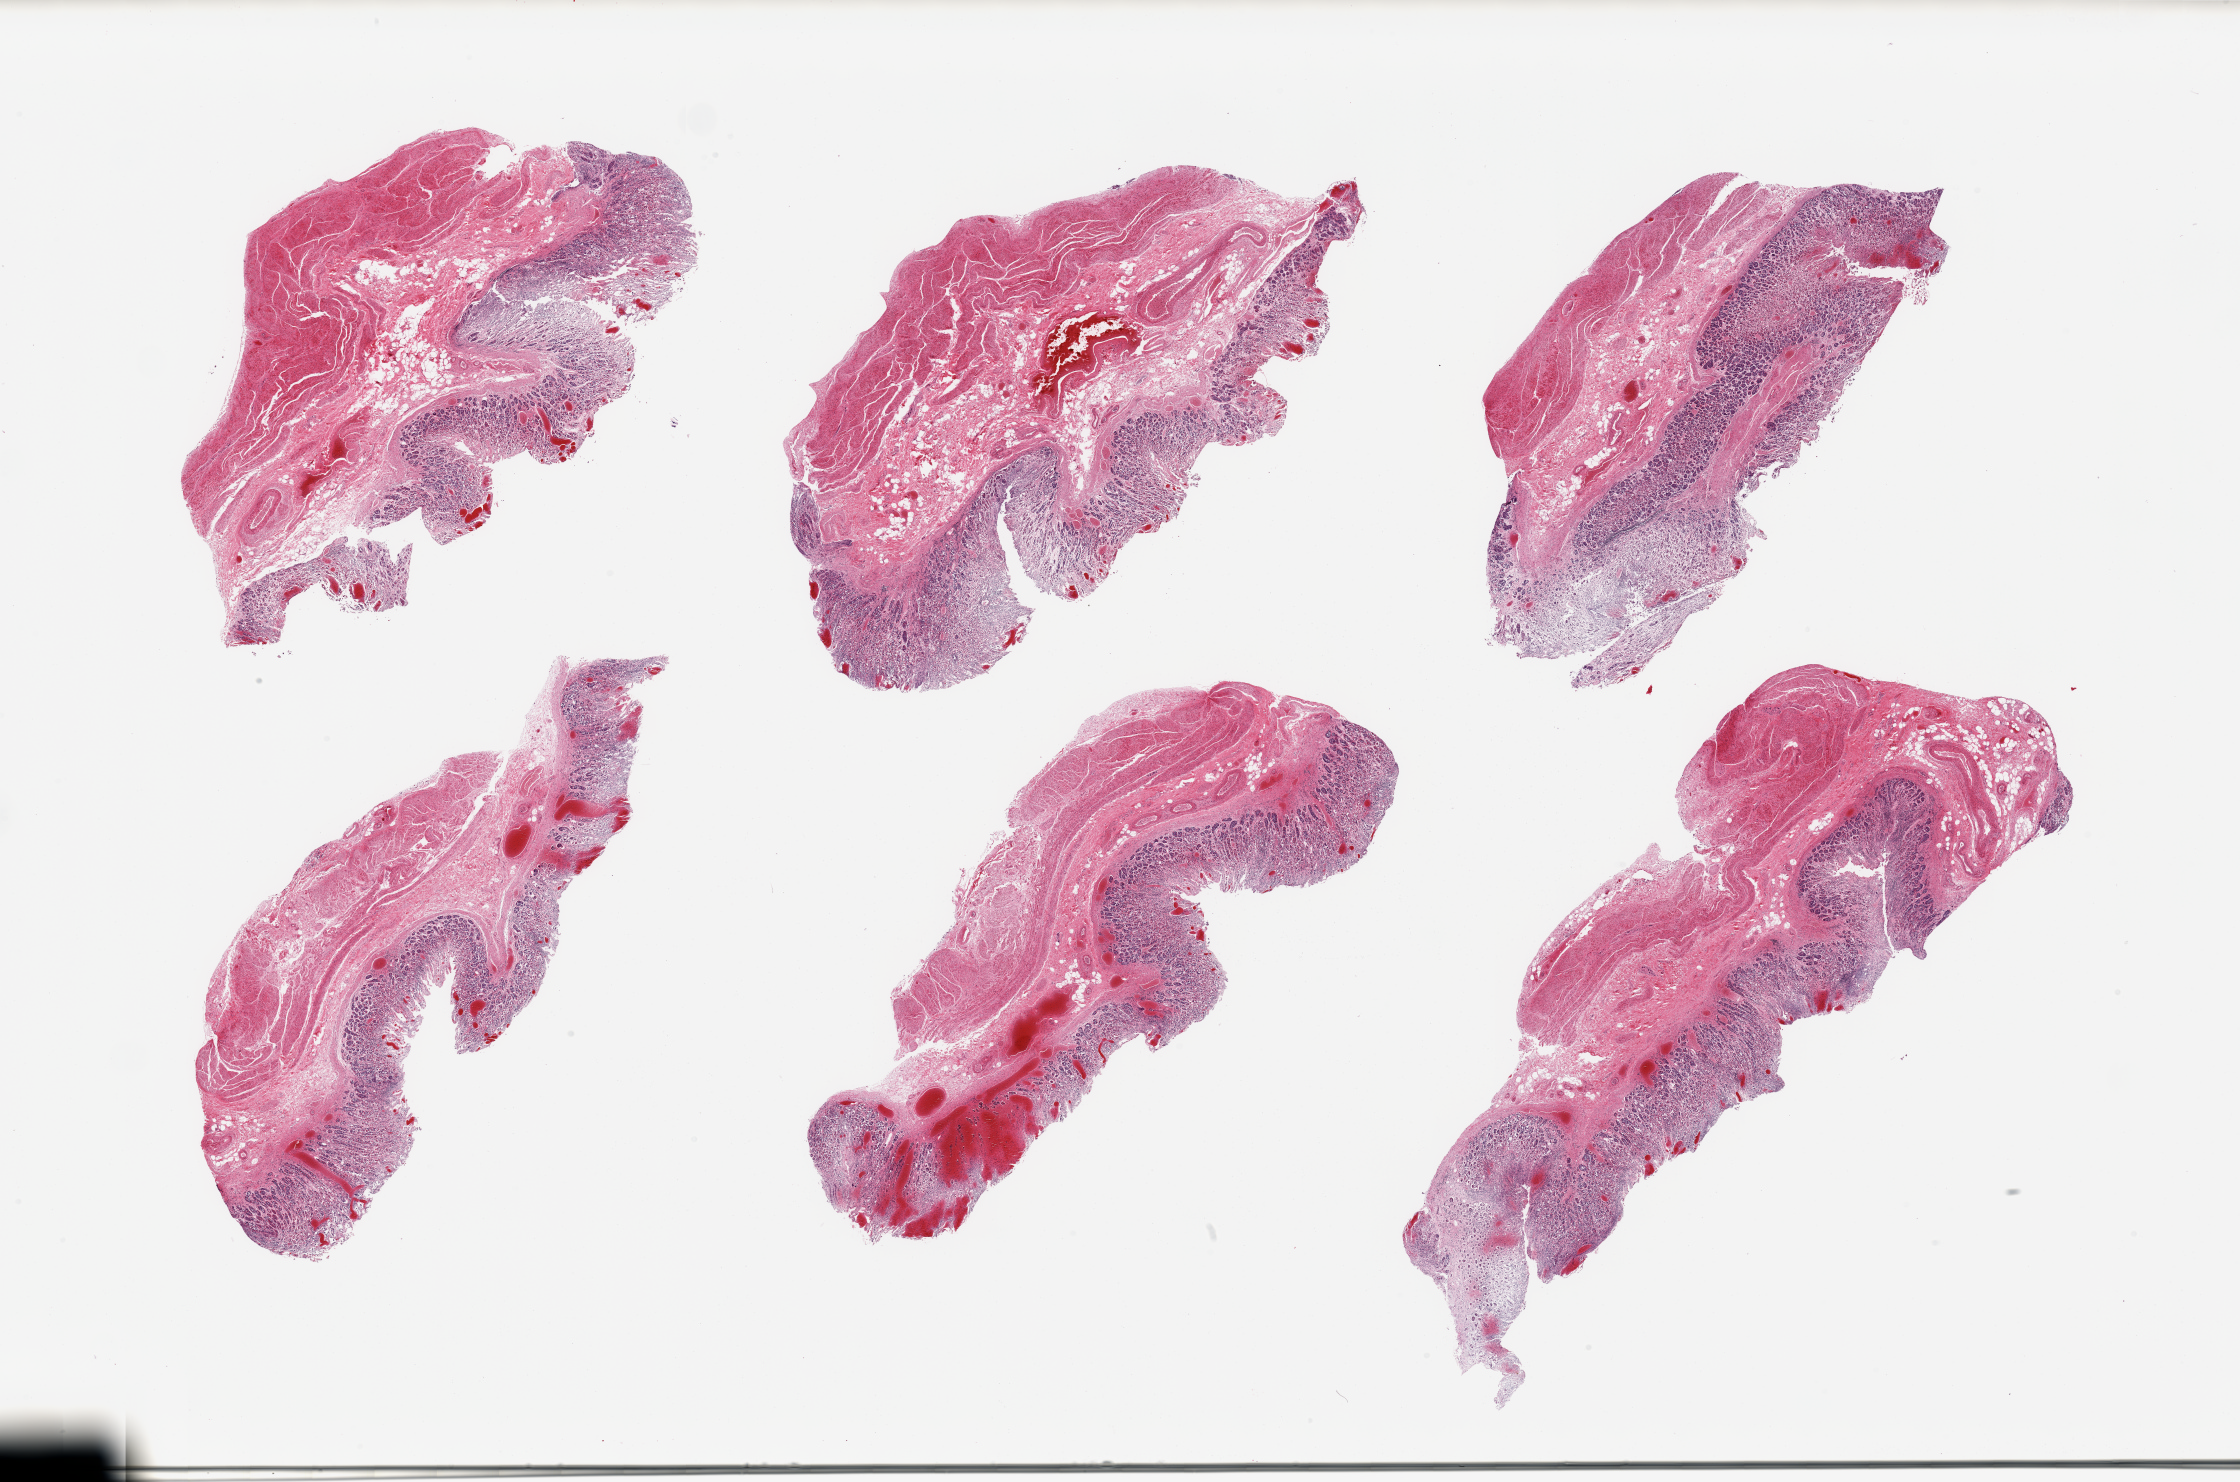
Whole-slide image, H&E stain, brightfield — whole scanned area (about 35.4 x 23.4 mm, slide scanned at 20x) shown as a low-resolution overview, PAXgene-fixed paraffin-embedded (PFPE) section, sampled site (target tissue): stomach, donor tissue sample. Donor: male.
Pathologist's review note for this sample: 6 pieces; moderately to severely autolyzed gastric mucosa and marked congestion; well preserved muscularis.